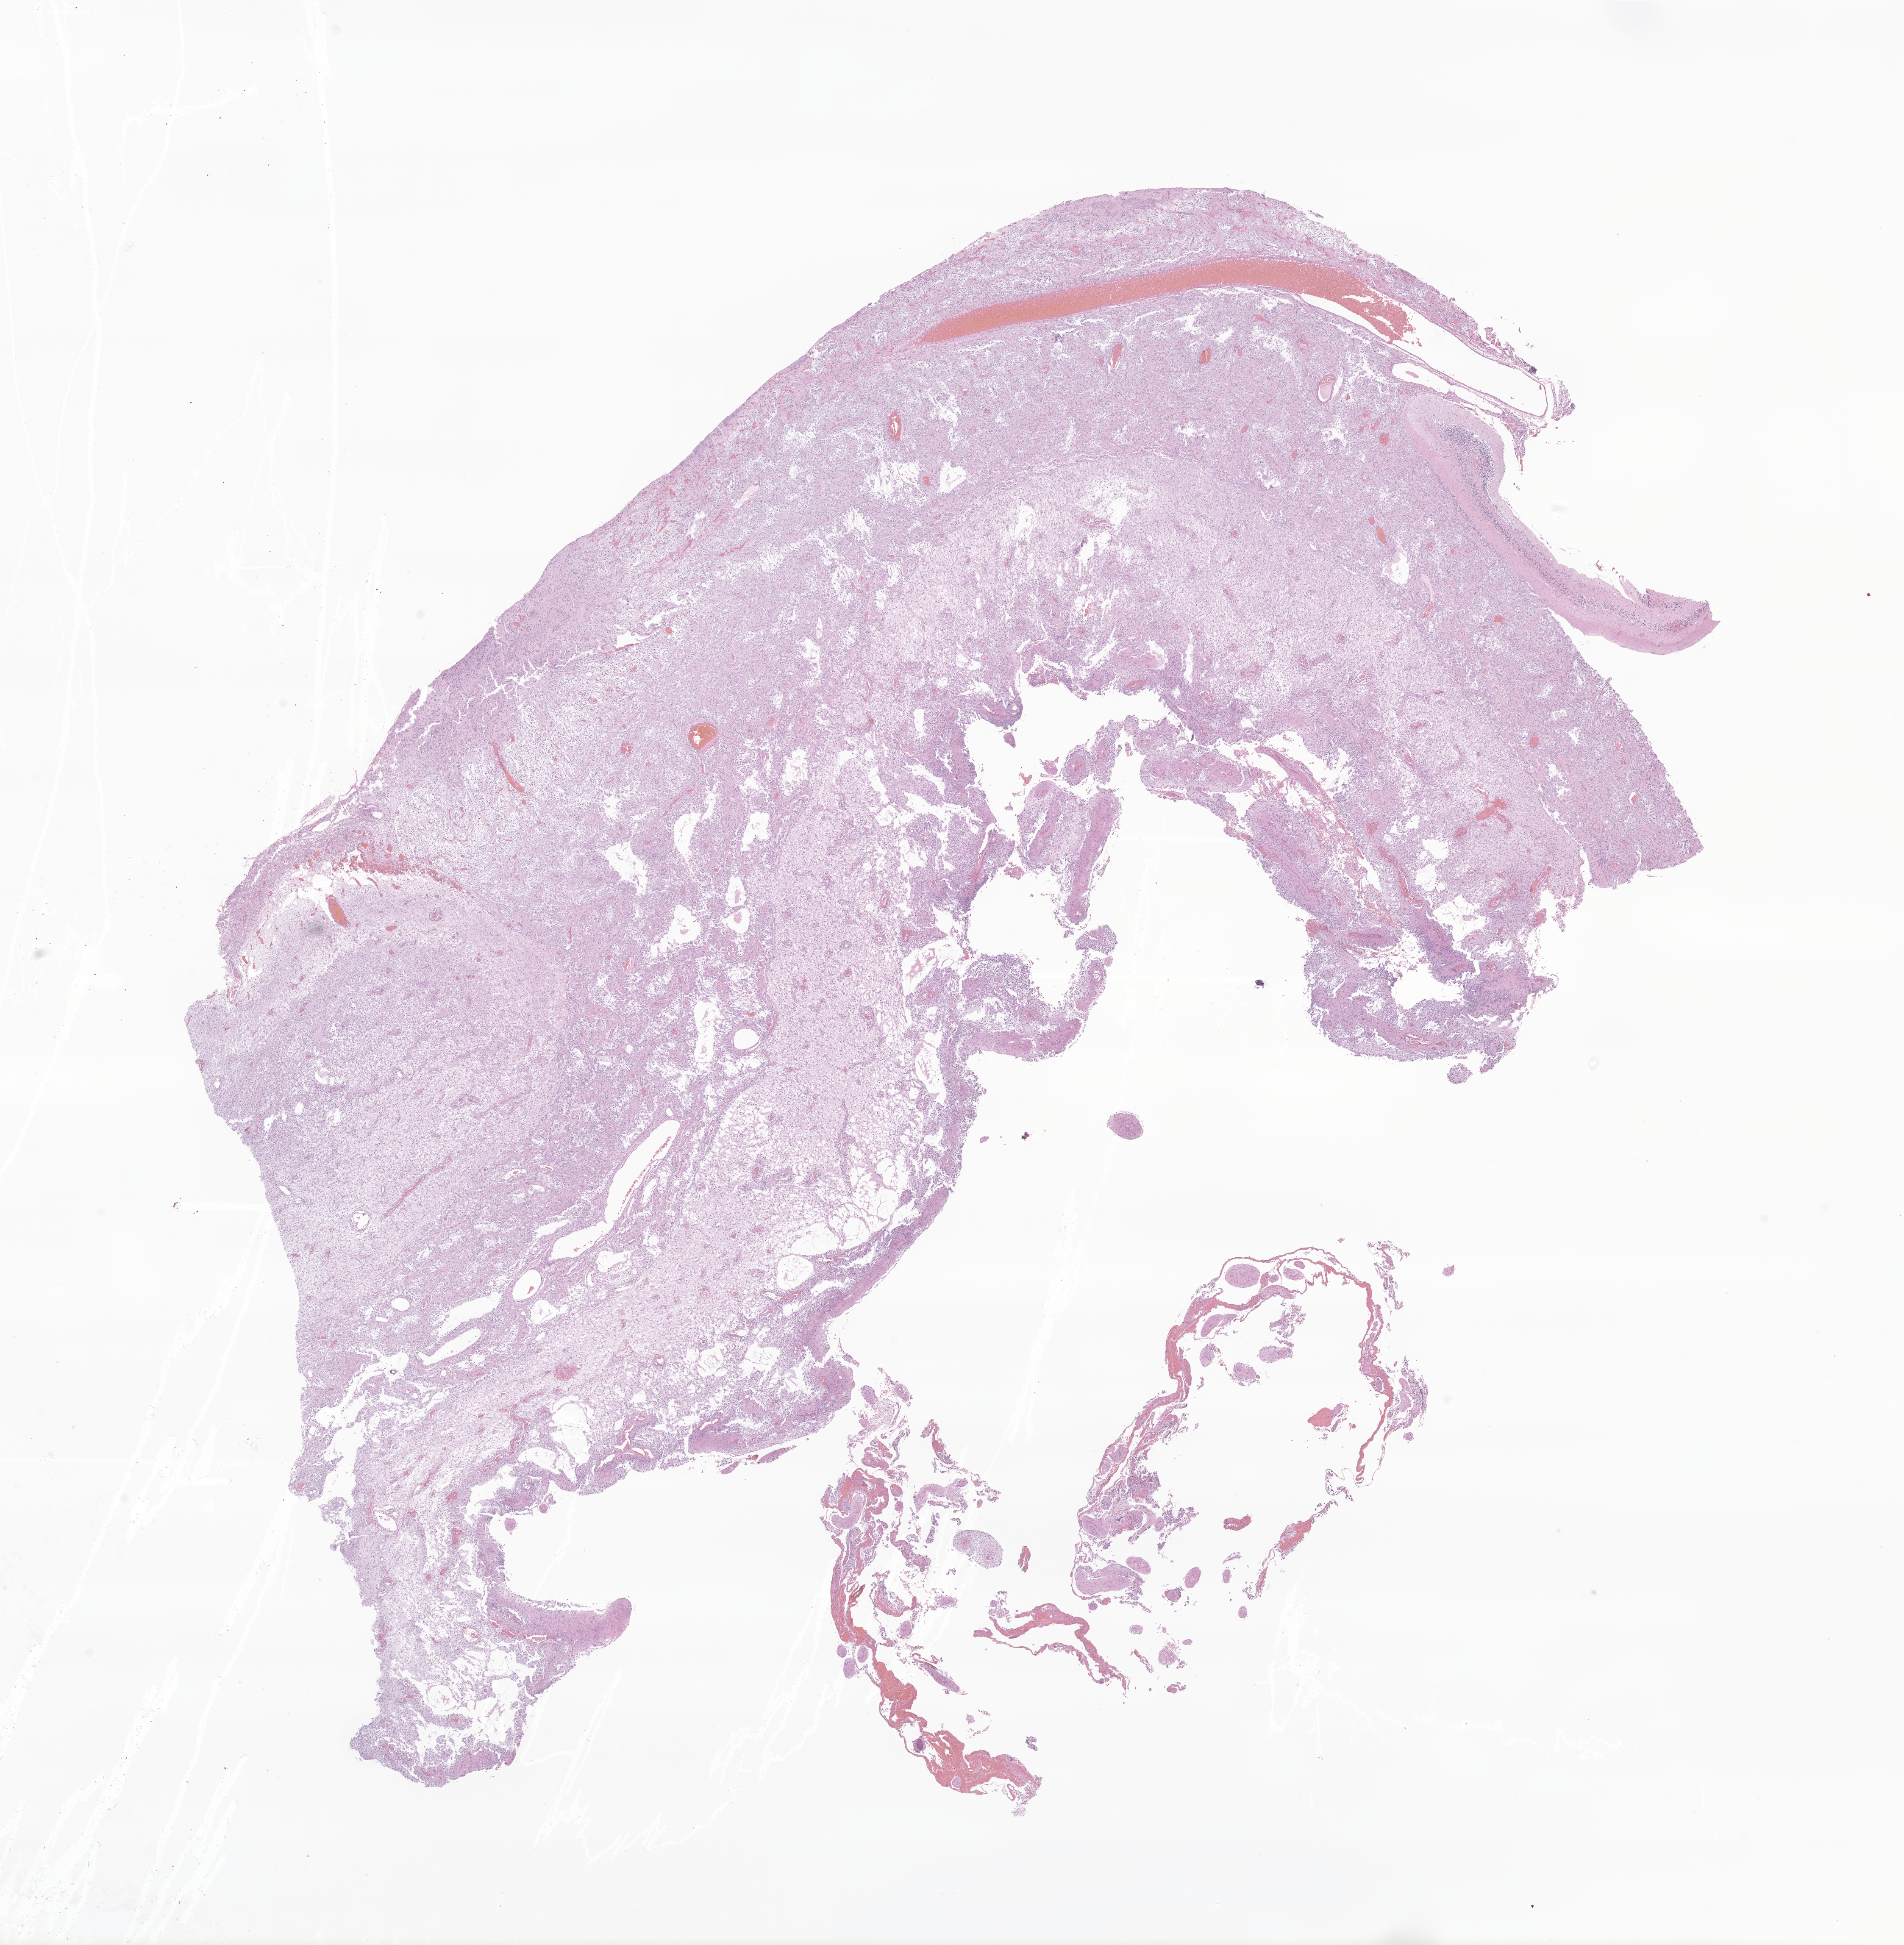
Whole-slide image, hematoxylin and eosin (H&E) stain of tumor tissue from the brain, whole scanned area (about 18.9 x 19.3 mm) shown as a low-resolution overview, FFPE section. Patient: male, age 858 days (about 2.3 years).
- diagnosis (ICD-O-3 morphology term): Neoplasm, malignant